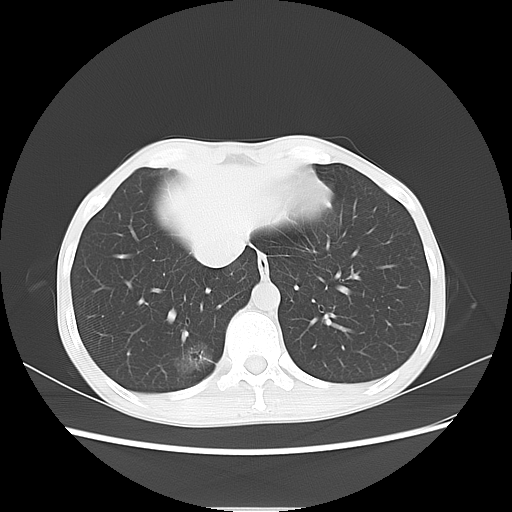
Chest CT, one axial slice. Position 20 of 69 along the scan axis. Reconstruction kernel LUNG. 120 kVp. Lung window (W 1500 / L -600 HU). 512 × 512 image matrix, field of view 350 × 350 mm. Female patient, age 51 years. Case-level facts recorded for this patient, not image findings: clinical TNM (as recorded): T1c N0 M0.
Outlined on this slice (bounding box drawn by a radiologist):
- lung tumour (recorded histology: adenocarcinoma): box from (x=165, y=333) to (x=217, y=383) px